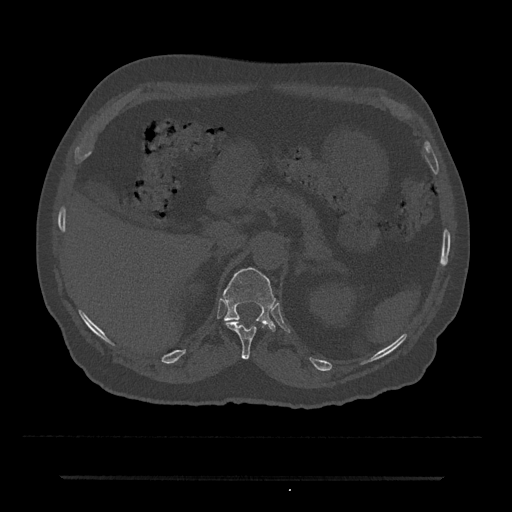
CT including the spine, one axial slice; position 150 of 797 along the scan axis; reconstruction kernel Br40s/3; bone window (W 1800 / L 400 HU); 0.5 mm slice thickness; 512 × 512 image matrix, field of view 437 × 437 mm. Patient: male, 69 years. From the clinical record (not read from this slice): primary cancer: prostate.
Annotated regions visible in this slice (semi-automatically segmented with operator editing):
- T11 vertebra: box from (x=225, y=321) to (x=264, y=360) px
- T12 vertebra: (x=223, y=267)–(x=276, y=331)